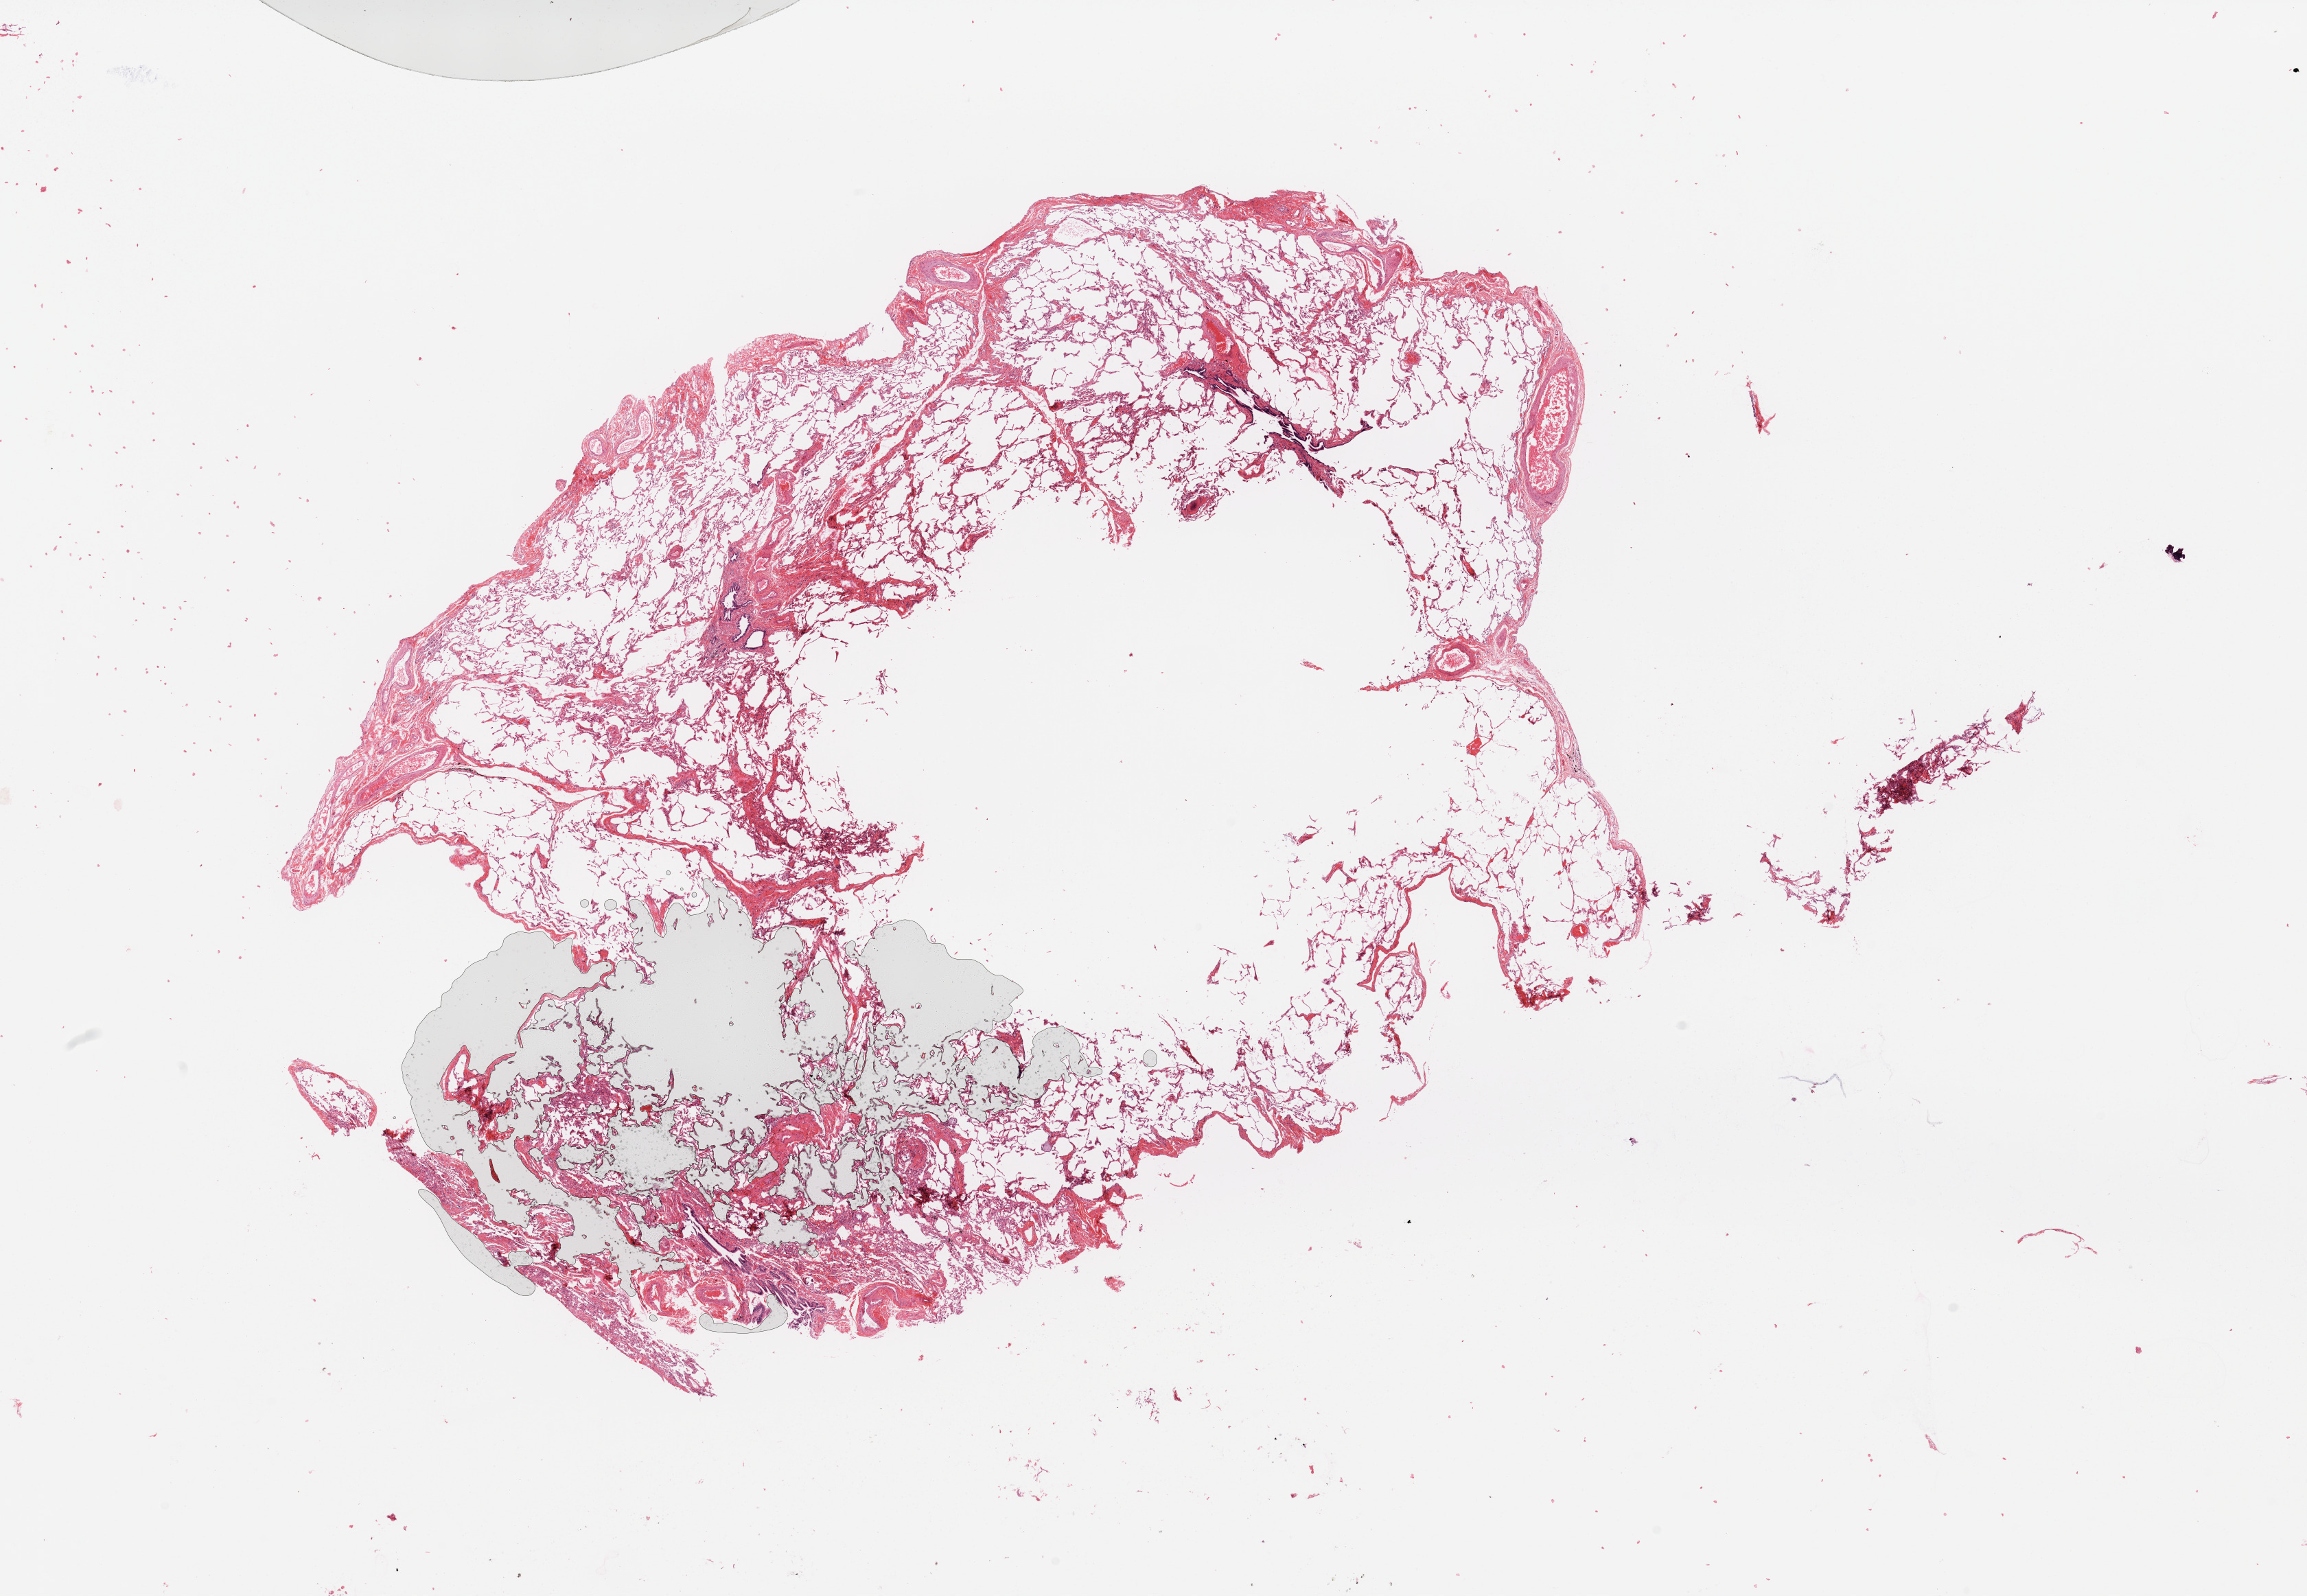
H&E-stained whole-slide image, shown as a low-resolution overview of the whole scanned area (about 26.6 x 18.4 mm), normal (non-tumour) tissue sample, sampled site: lung. Male, 59 y/o.
This section: normal (non-tumour) tissue from the same patient. Patient diagnosis: Squamous cell carcinoma, NOS.